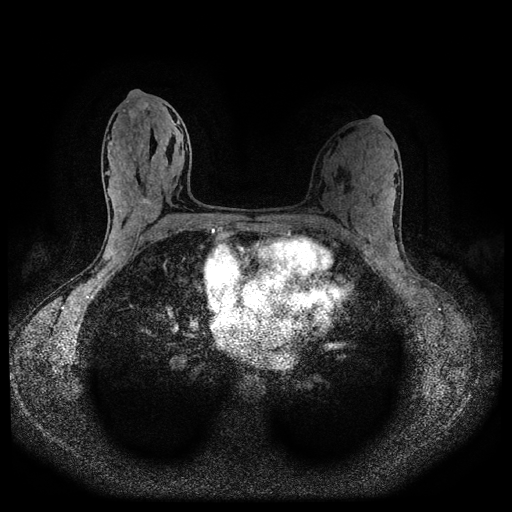
Breast MRI (dynamic contrast-enhanced, multi-phase), one axial slice. Slice 57 of 116 in the series (ordered by position). Dynamic contrast-enhanced series, time point 2 of 5 at this slice position (early post-contrast). 1.5 T. TE 2.7 ms, TR 5.4 ms. 512 × 512 image matrix, field of view 330 × 330 mm. Female patient, age 32 years.
Structures marked on this image (semi-automatic segmentation, software-assisted and operator-edited):
- breast lesion (labelled benign in the annotation): box from (x=129, y=102) to (x=150, y=118) px